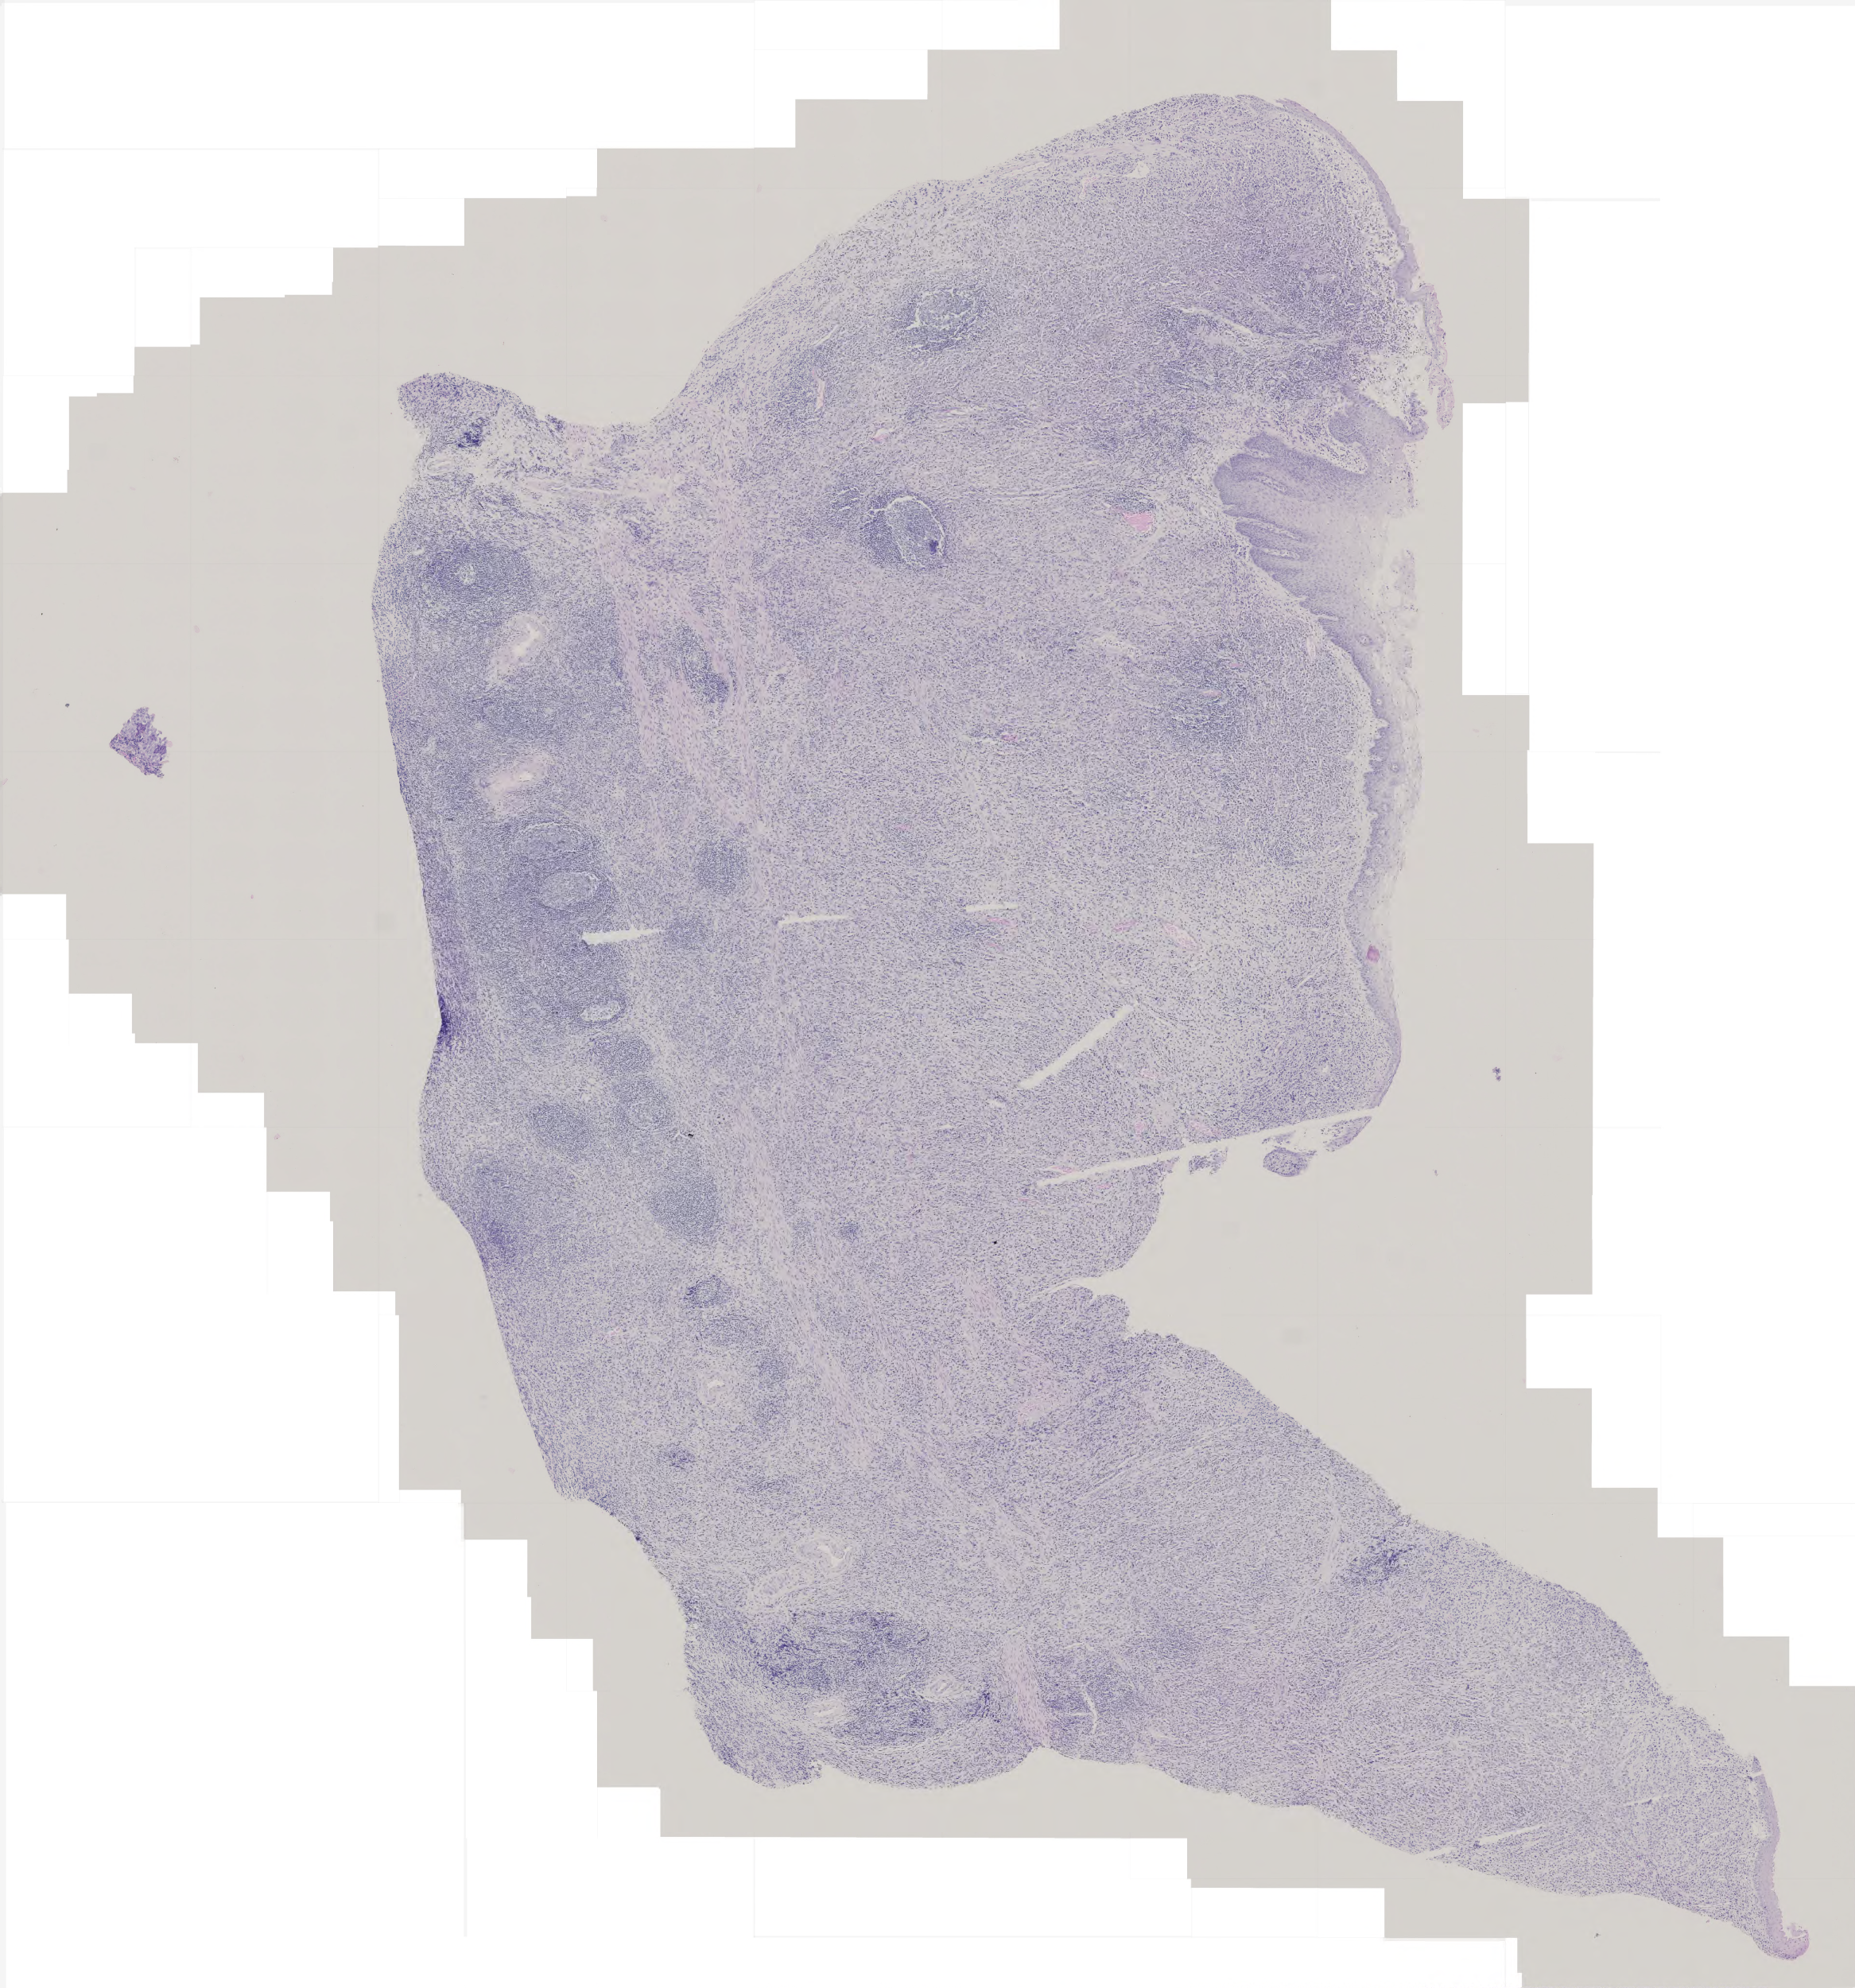
H&E-stained whole-slide image — whole scanned area (about 4.7 x 5.0 mm) shown as a low-resolution overview, formalin-fixed paraffin-embedded (FFPE) diagnostic section, sample: primary tumour, stomach. Male, age 58 years at initial diagnosis. Histologic grade: G3 (poorly differentiated).
Diagnosis: Adenocarcinoma, intestinal type (cardia, NOS). AJCC pathologic stage: II (6th edition). Lymph nodes positive (case pathology): 3 of 26 examined.